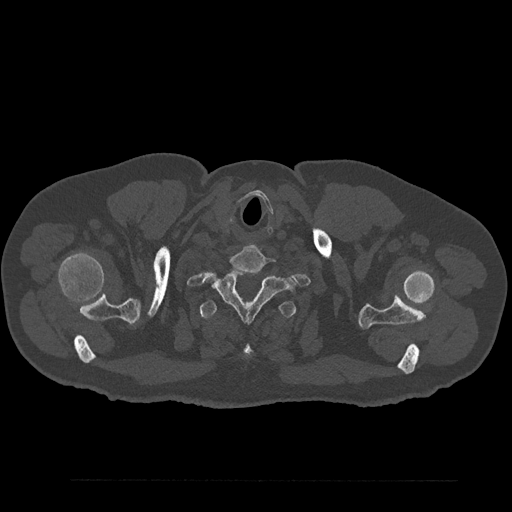
CT including the spine, one axial slice. Position 750 of 797 along the scan axis. 120 kVp. Bone window (W 1800 / L 400 HU). 512 × 512 image matrix, field of view 430 × 430 mm. Patient: male, 61 years. Case-level facts recorded for this patient, not image findings: primary cancer: prostate.
Structures marked on this image (semi-automatic segmentation, software-assisted and operator-edited):
- T1 vertebra: bounding box <208,269,295,322> (left, top, right, bottom; pixels)
- T2 vertebra: <200,299,296,359>